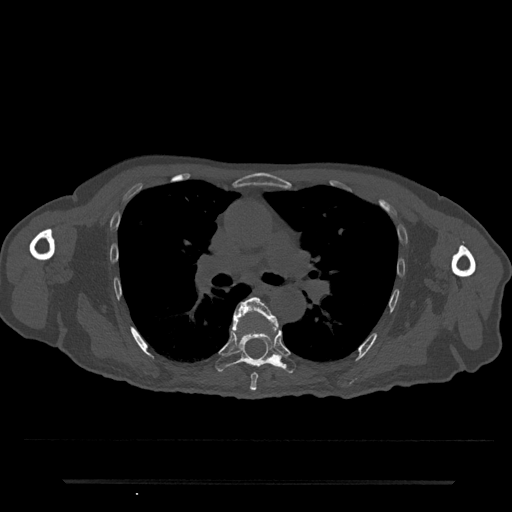
CT including the spine, one axial slice; position 499 of 797 along the scan axis; reconstruction kernel Br40s/3; 120 kVp; bone window (W 1800 / L 400 HU); 0.5 mm slice thickness; 512 × 512 image matrix, field of view 427 × 427 mm. Male patient, age 74 years. From the clinical record (not read from this slice): primary cancer: prostate.
Outlined on this slice (semi-automatically segmented with operator editing):
- T6 vertebra: bounding box [x1, y1, x2, y2] px = [232, 297, 279, 391]
- T7 vertebra: [215, 328, 296, 373]